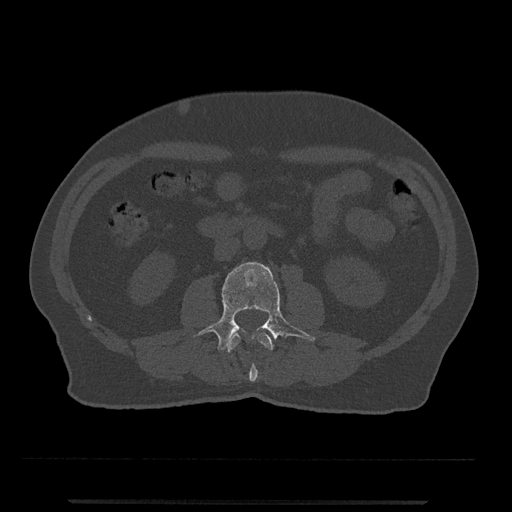
CT including the spine, one axial slice; position 215 of 797 along the scan axis; 120 kVp; bone window (W 1800 / L 400 HU); 0.5 mm slice thickness; 512 × 512 image matrix. Patient: male, 63 years. From the clinical record (not read from this slice): primary cancer: prostate.
Annotated regions visible in this slice (semi-automatically segmented with operator editing):
- L2 vertebra: bounding box <227,332,273,382> (left, top, right, bottom; pixels)
- L3 vertebra: <196,262,315,351>